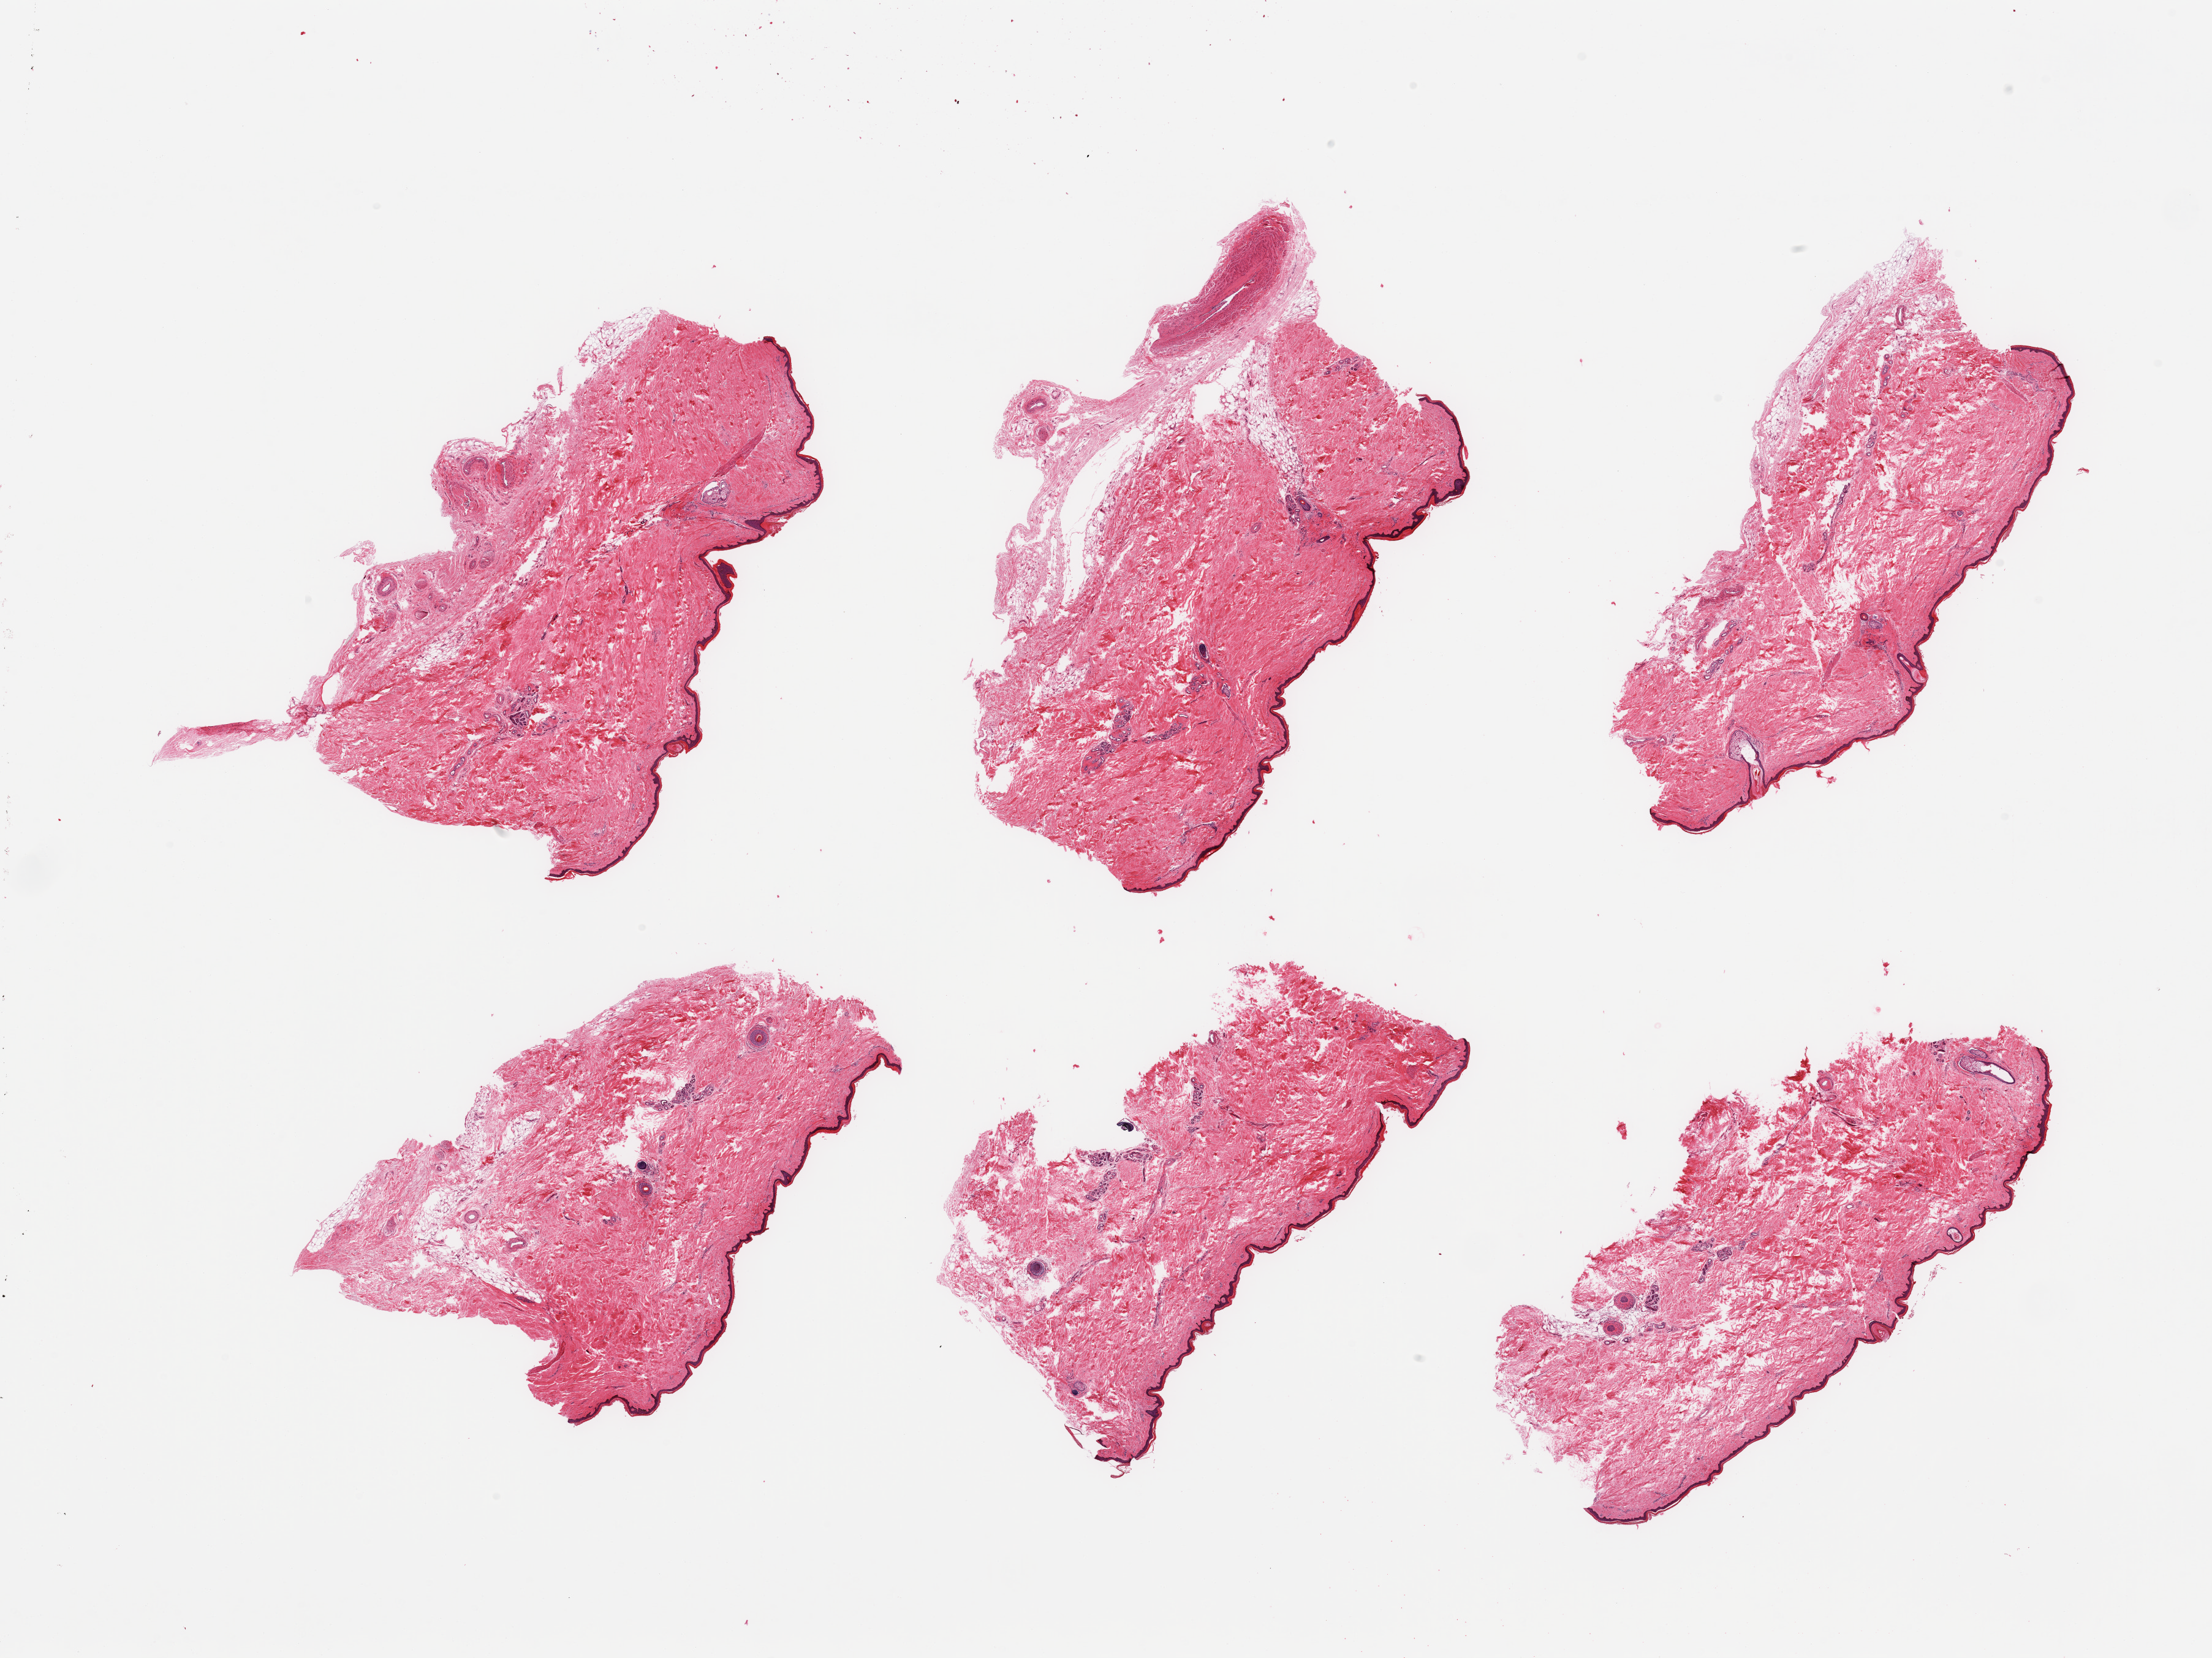
Whole-slide image, haematoxylin and eosin stain — shown as a low-resolution overview of the whole scanned area (about 28.5 x 21.4 mm, slide scanned at 20x), PAXgene-fixed paraffin-embedded (PFPE) section, section of skin of lower leg (target tissue), tissue donor sample. Donor: male.
* pathologist's review note for this sample: 6 pieces, trace dermal fat ;squamous epithelium is ~30-40 microns